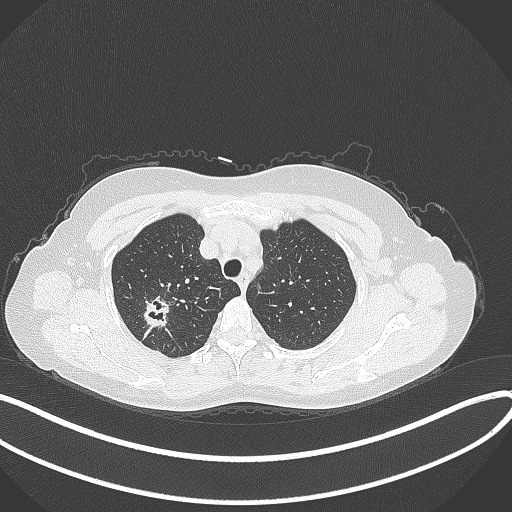
Chest CT, one axial slice. Position 295 of 337 along the scan axis. Reconstruction kernel B70f. 120 kVp. Lung window (W 1500 / L -600 HU). 512 × 512 image matrix. Female patient, age 50 years. From the clinical record (not read from this slice): clinical TNM (as recorded): T1c N0 M0.
Annotated regions visible in this slice (bounding box drawn by a radiologist):
- lung tumour (recorded histology: adenocarcinoma): bounding box [x1, y1, x2, y2] px = [137, 289, 171, 332]